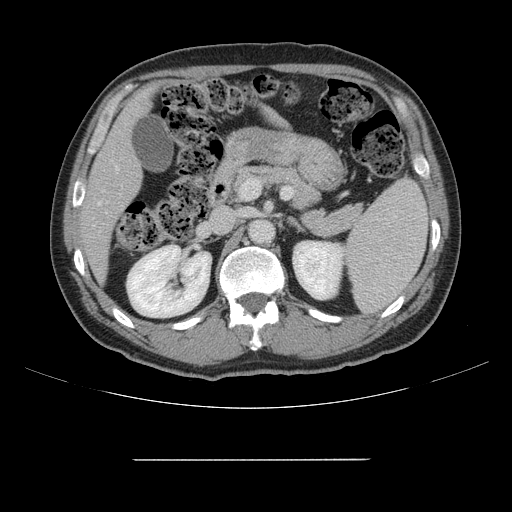
Contrast-enhanced abdominal CT, one axial slice. Slice 76 of 164 in the series (ordered by position). Soft-tissue window (W 400 / L 40 HU). 2.5 mm slice thickness. 512 × 512 image matrix, field of view 404 × 404 mm. Male patient, age 54 years. From the clinical record (not read from this slice): diagnosis: colorectal cancer liver metastases, imaged before liver resection; multiple liver metastases: yes; largest metastasis: 1 cm; disease in both lobes: no.
Outlined on this slice (expert manual segmentation):
- hepatic veins: bounding box (x1, y1, x2, y2) in pixels: (98, 167, 118, 205)
- liver: (85, 93, 148, 278)
- planned liver remnant (the part of the liver to remain after resection): (85, 92, 150, 278)